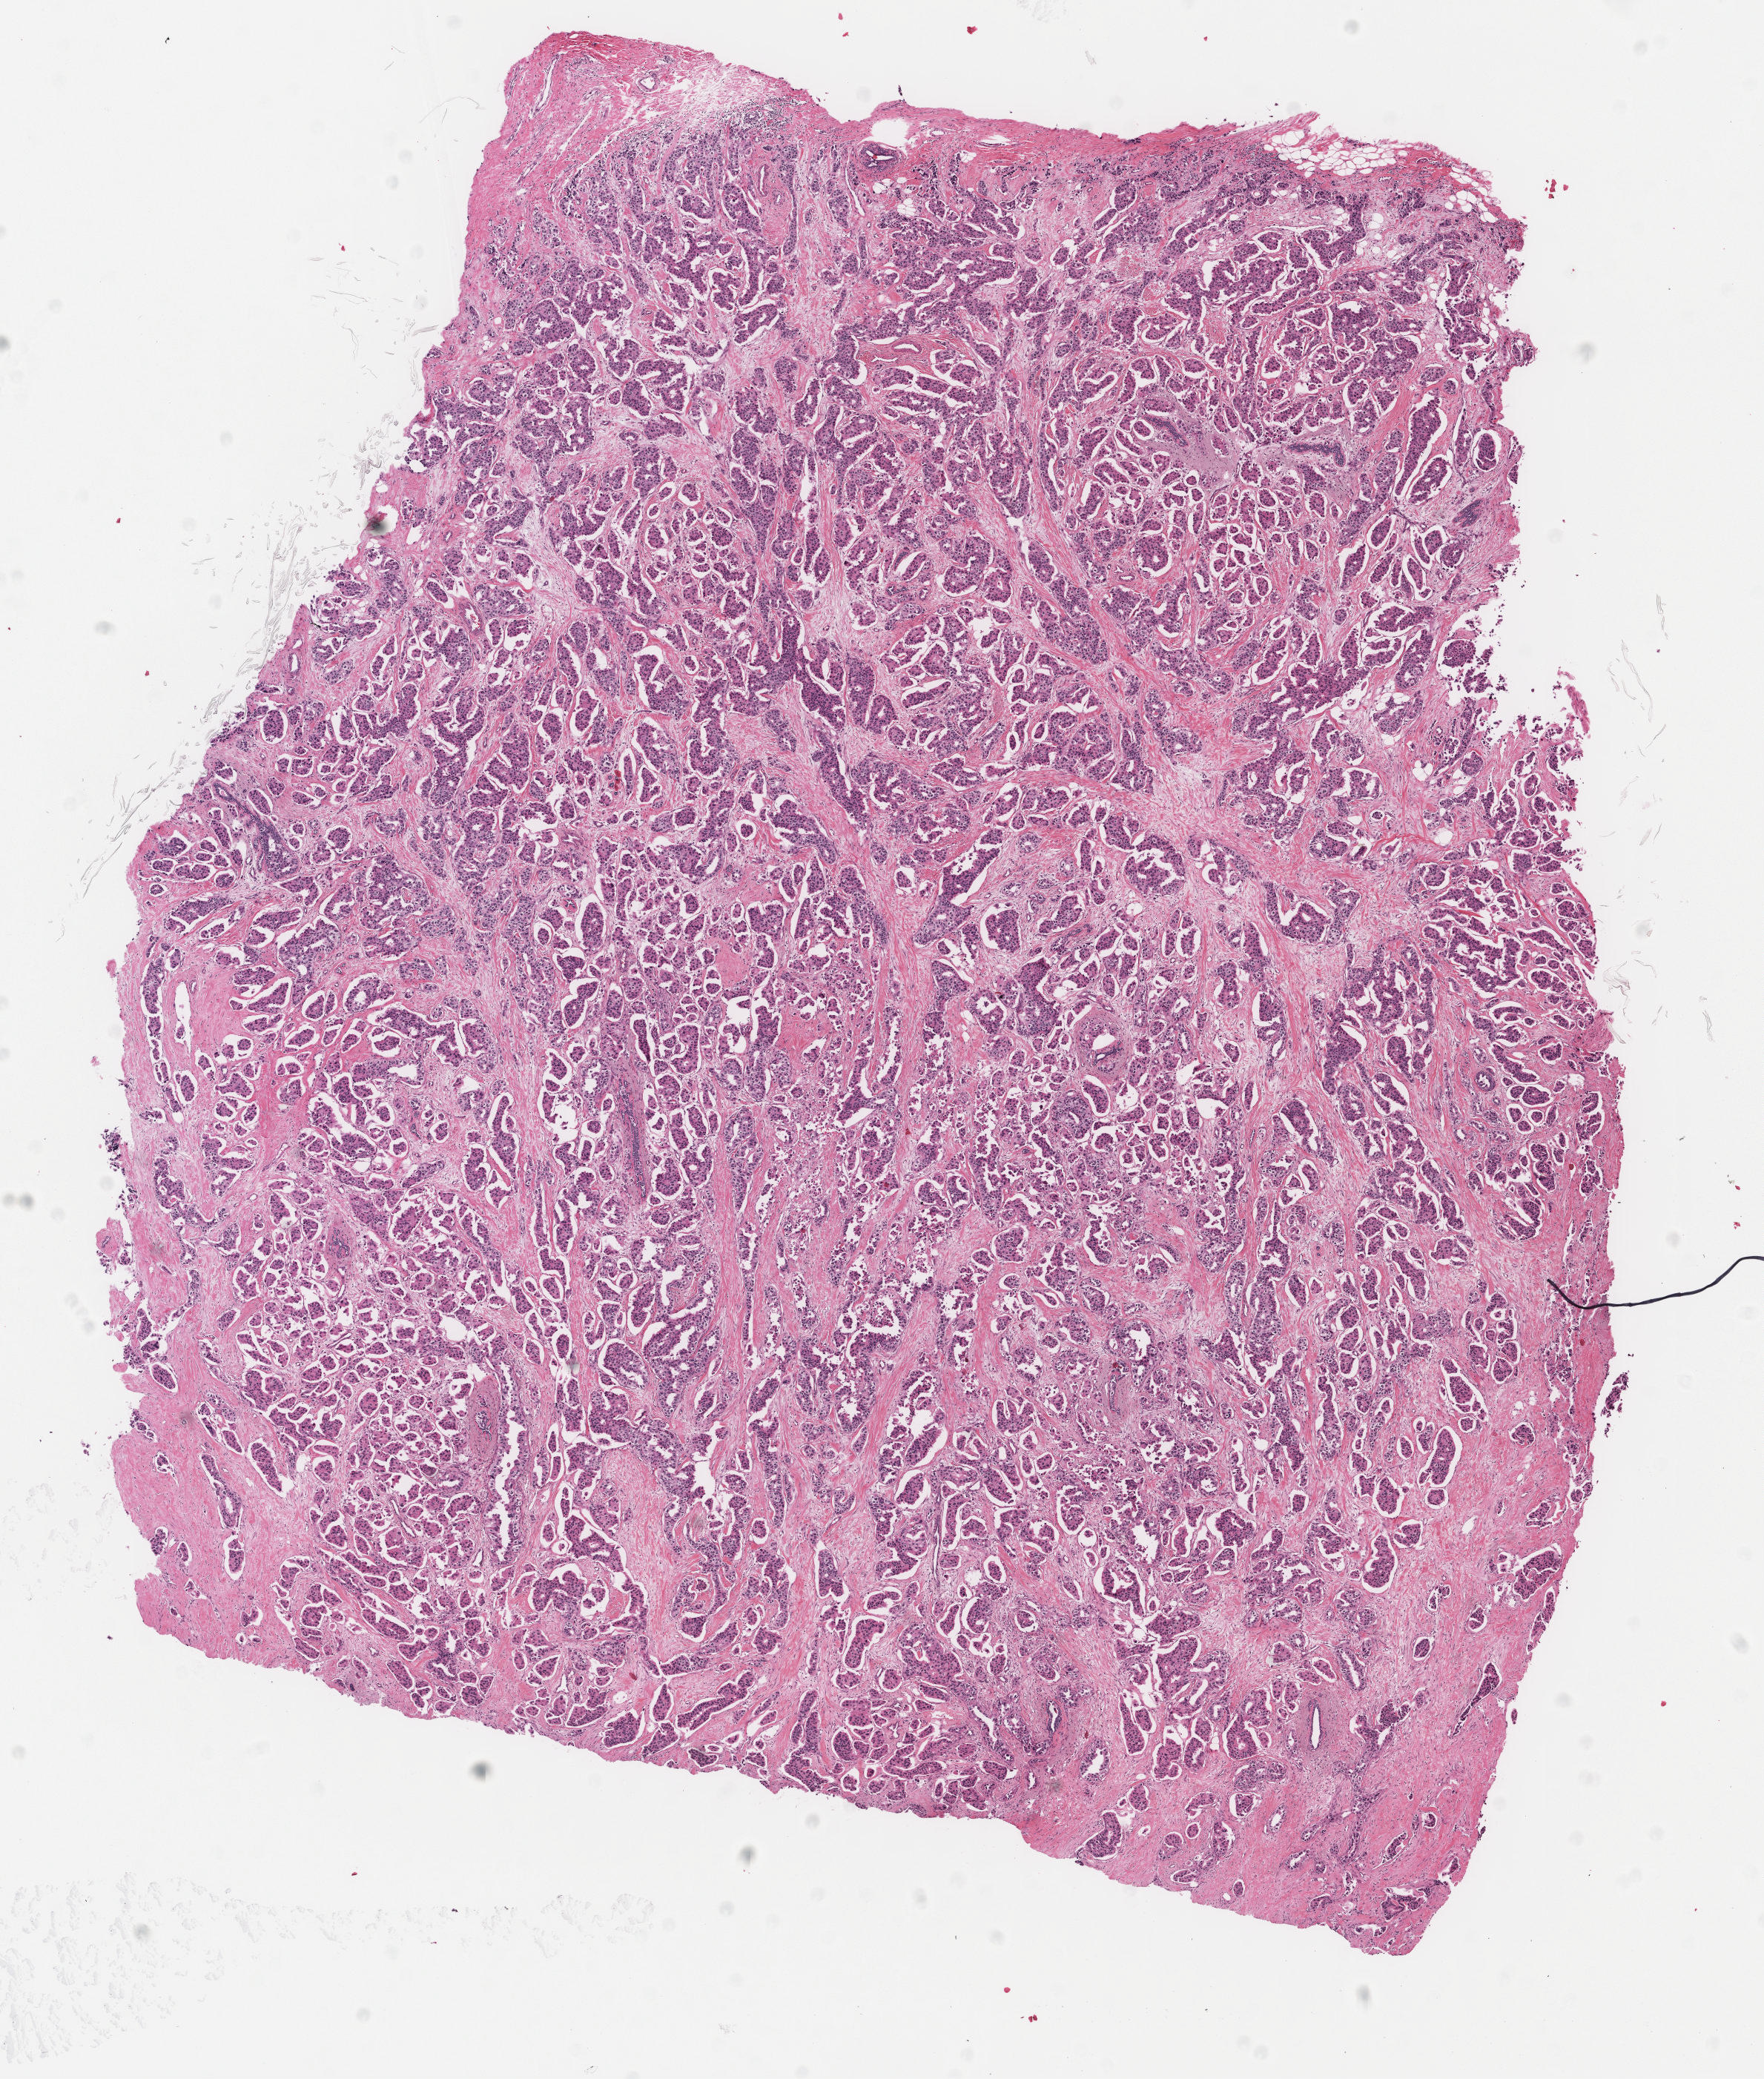
H&E-stained whole-slide image — shown as a low-resolution overview of the whole scanned area (about 9.4 x 11.1 mm), formalin-fixed paraffin-embedded (FFPE) diagnostic section, sample: primary tumour, breast. Female, age 45 years at initial diagnosis.
Laterality: left. Lymph nodes positive (case pathology): 1 of 14 examined. Histologic diagnosis: Infiltrating duct carcinoma, NOS. AJCC pathologic stage: IIIA.